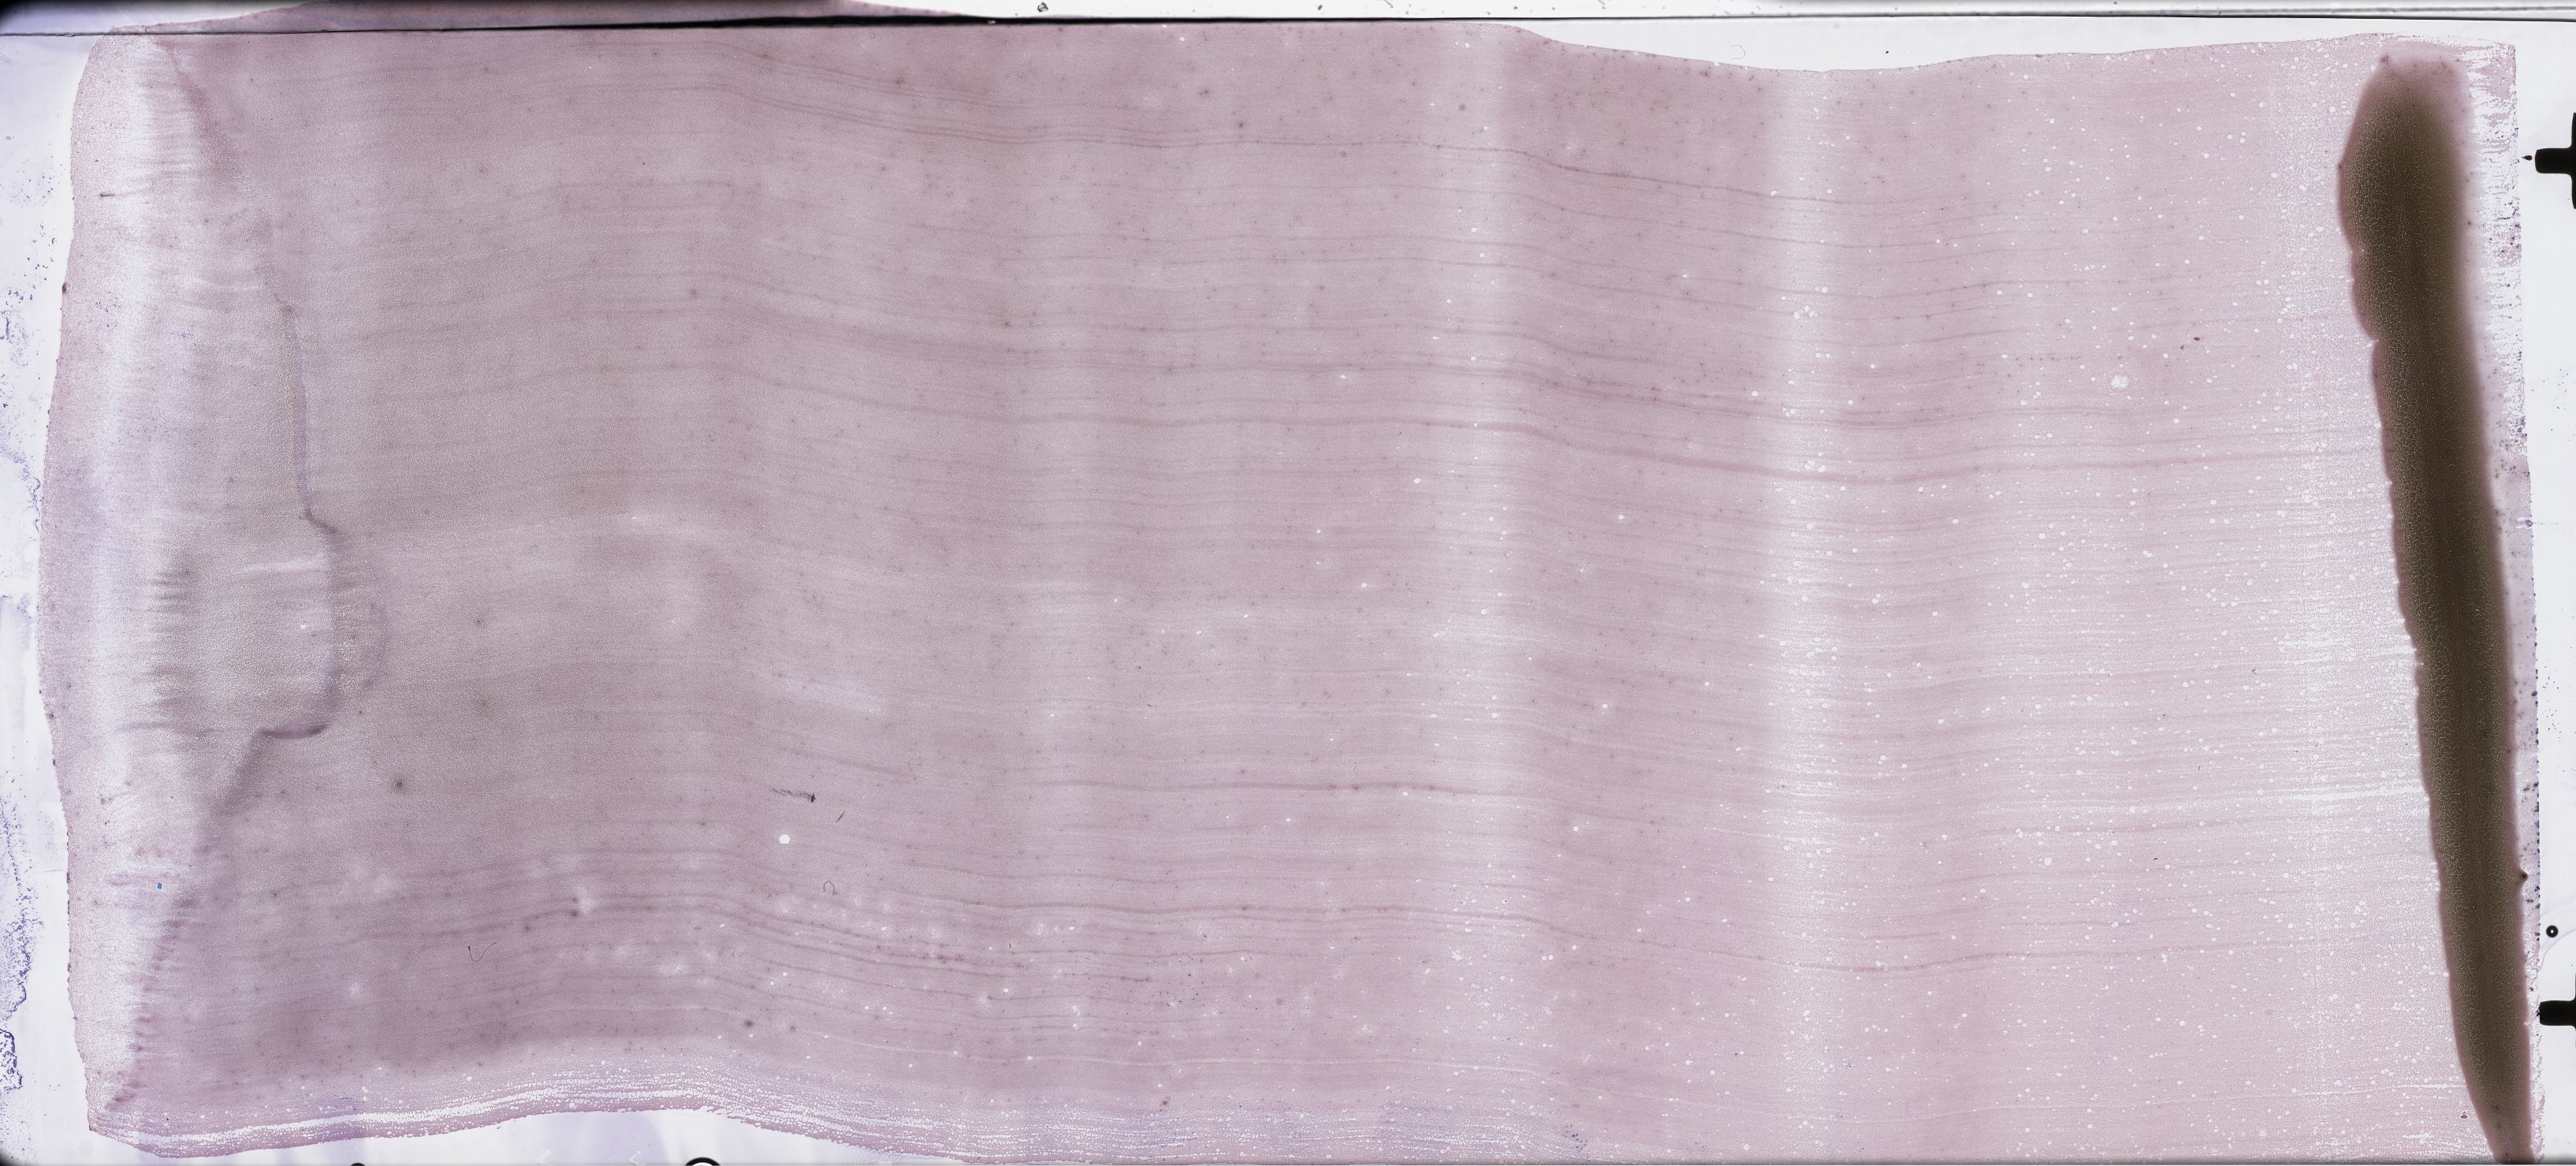
Whole-slide image of a whole blood smear, Wright-Giemsa stain — shown as a low-resolution overview of the whole scanned area (about 52.8 x 23.9 mm). EDTA-anticoagulated smear. Specimen time point: collected at baseline (before treatment). Patient sex: male.
- from a patient with: Plasma Cell Myeloma